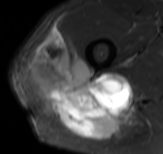
MRI of an extremity soft-tissue mass, one axial slice. Slice 56 of 61 in the series (ordered by position). STIR. MR volume resampled by the dataset authors to the PET/CT grid (not the native acquisition matrix). 3.27 mm slice thickness. 163 × 154 image matrix, field of view 159 × 150 mm. Male patient. Case-level facts recorded for this patient, not image findings: histological type: poorly differentiated synovial sarcoma; grade: high; site of the primary tumour: right buttock.
Structures marked on this image (expert contour drawn on MRI and transferred to this co-registered scan by the dataset authors):
- gross tumour volume including surrounding oedema: bounding box <23,28,145,140> (left, top, right, bottom; pixels)
- gross tumour volume (mass): <23,28,131,140>